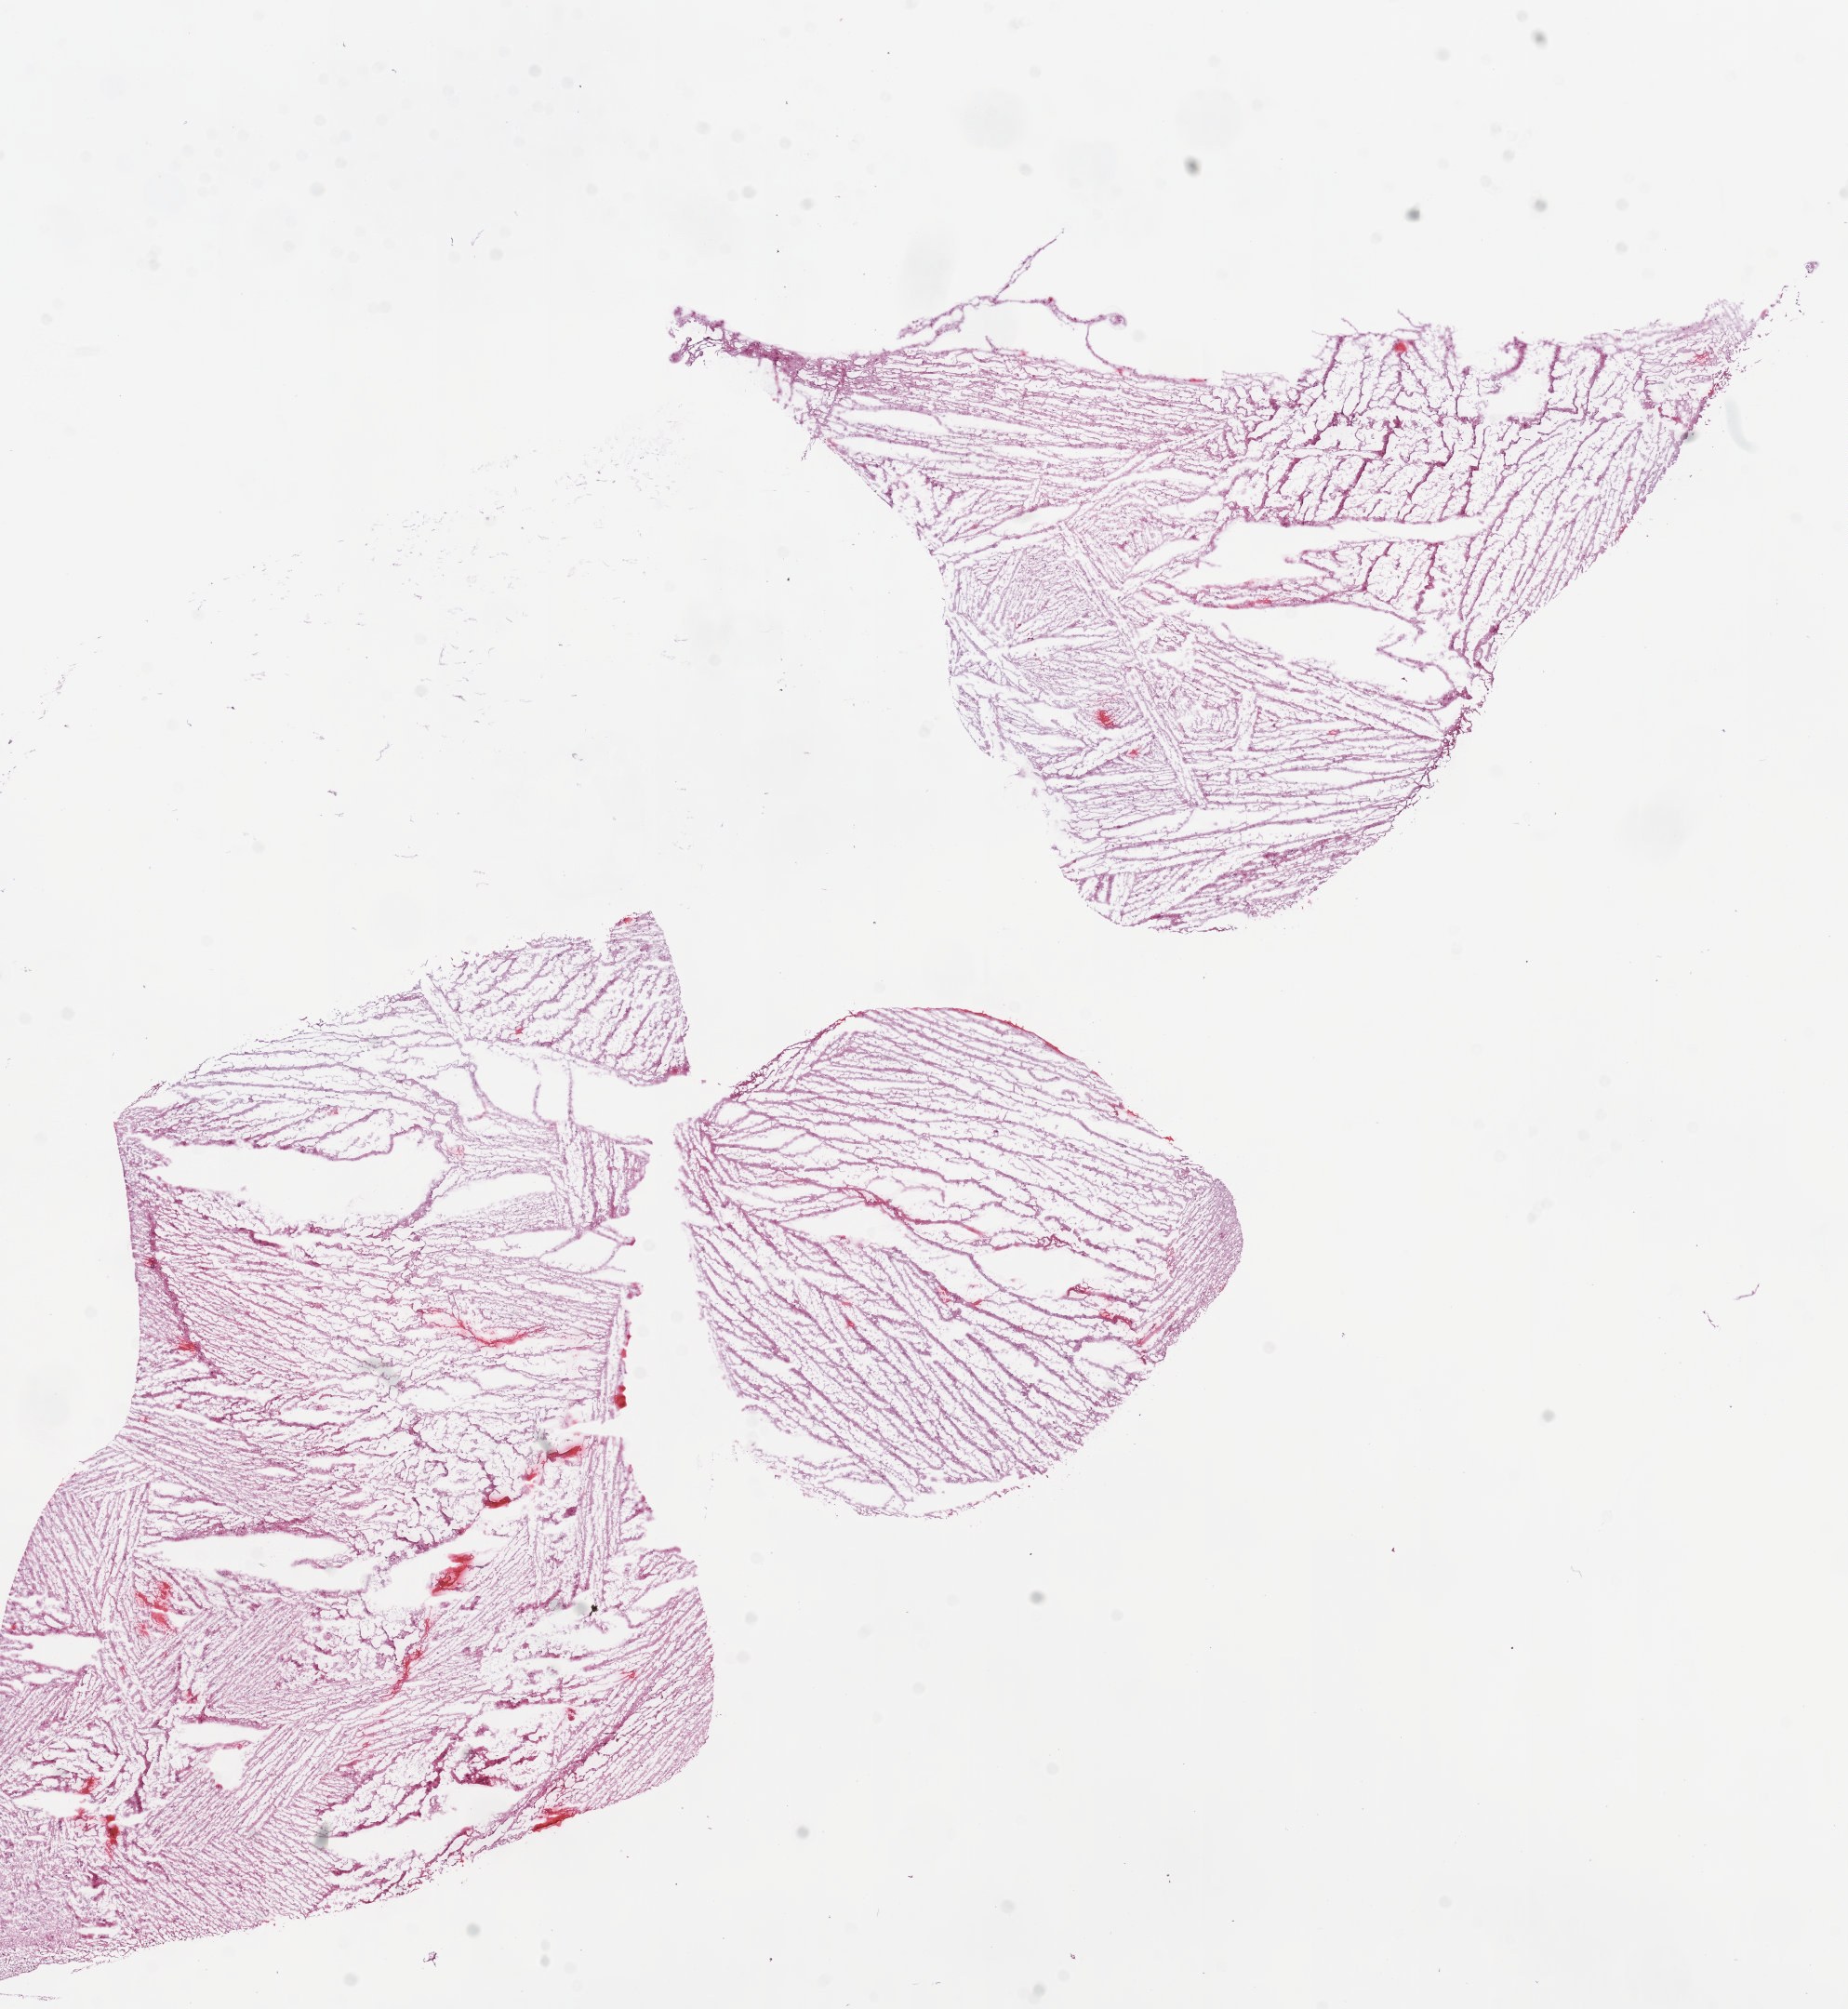
Hematoxylin and eosin (H&E) stained whole-slide image, shown as a low-resolution overview of the whole scanned area (about 15.9 x 17.3 mm, slide scanned at 5x); frozen section from the top of the tissue portion; primary tumour sample from the brain. Male, age 43 years at initial diagnosis. Histologic grade: G2 (moderately differentiated). Pathologist review of this section (percent, as recorded): tumour cells 100%, tumour nuclei 75%, normal cells 0%, stromal cells 0%, necrosis 0%.
Laterality: right. Diagnosis: Mixed glioma.